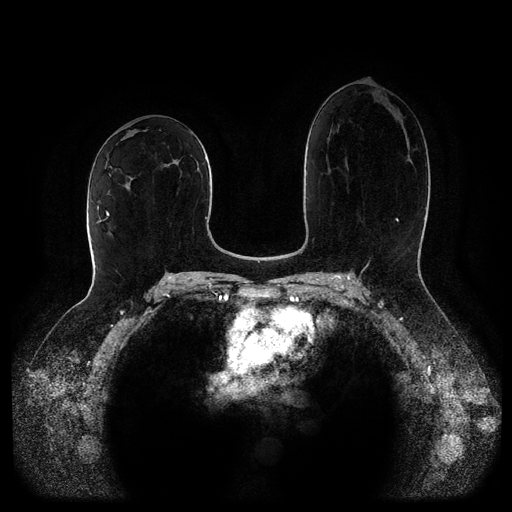
Breast MRI (dynamic contrast-enhanced, multi-phase), one axial slice; slice 52 of 116 in the series (ordered by position); dynamic contrast-enhanced series, time point 2 of 5 at this slice position (early post-contrast); 1.5 T; TE 2.6 ms, TR 5.2 ms; 2 mm slice thickness; 512 × 512 image matrix. Female patient, age 52 years.
Outlined on this slice (semi-automatic segmentation, software-assisted and operator-edited):
- breast lesion (labelled 'tumour' in the annotation; benign lesions carry a separate 'benign' label): bounding box [x1, y1, x2, y2] px = [163, 159, 184, 167]